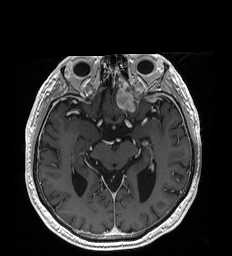
Brain MRI from a brain-tumour surgery series, one axial slice. Slice 115 of 192 in the series (ordered by position). T1-weighted post-contrast. 1 mm slice thickness. 232 × 256 image matrix, field of view 227 × 250 mm. From the clinical record (not read from this slice): histopathology: Glioblastoma; WHO grade: 4; IDH mutation: no.
Annotated regions visible in this slice (outlined manually by an expert reader):
- tumour: bounding box <116,88,135,112> (left, top, right, bottom; pixels)